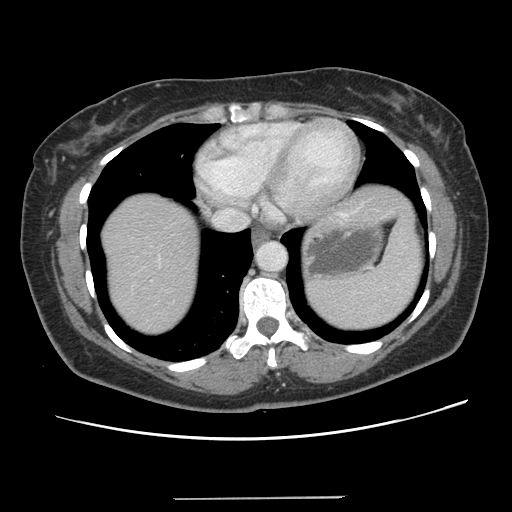
Contrast-enhanced abdominal CT, one axial slice. Position 121 of 141 along the scan axis. 120 kVp. Intravenous contrast given. Soft-tissue window (W 400 / L 40 HU). 2.5 mm slice thickness. 512 × 512 image matrix. Female patient, age 53 years. Case-level facts recorded for this patient, not image findings: diagnosis: colorectal cancer liver metastases, imaged before liver resection; multiple liver metastases: no; largest metastasis: 14.5 cm; chemotherapy before resection: yes.
Outlined on this slice (expert manual segmentation):
- hepatic veins: box from (x=138, y=208) to (x=244, y=272) px
- liver: (x=100, y=184)–(x=410, y=335)
- planned liver remnant (the part of the liver to remain after resection): (x=100, y=214)–(x=201, y=336)